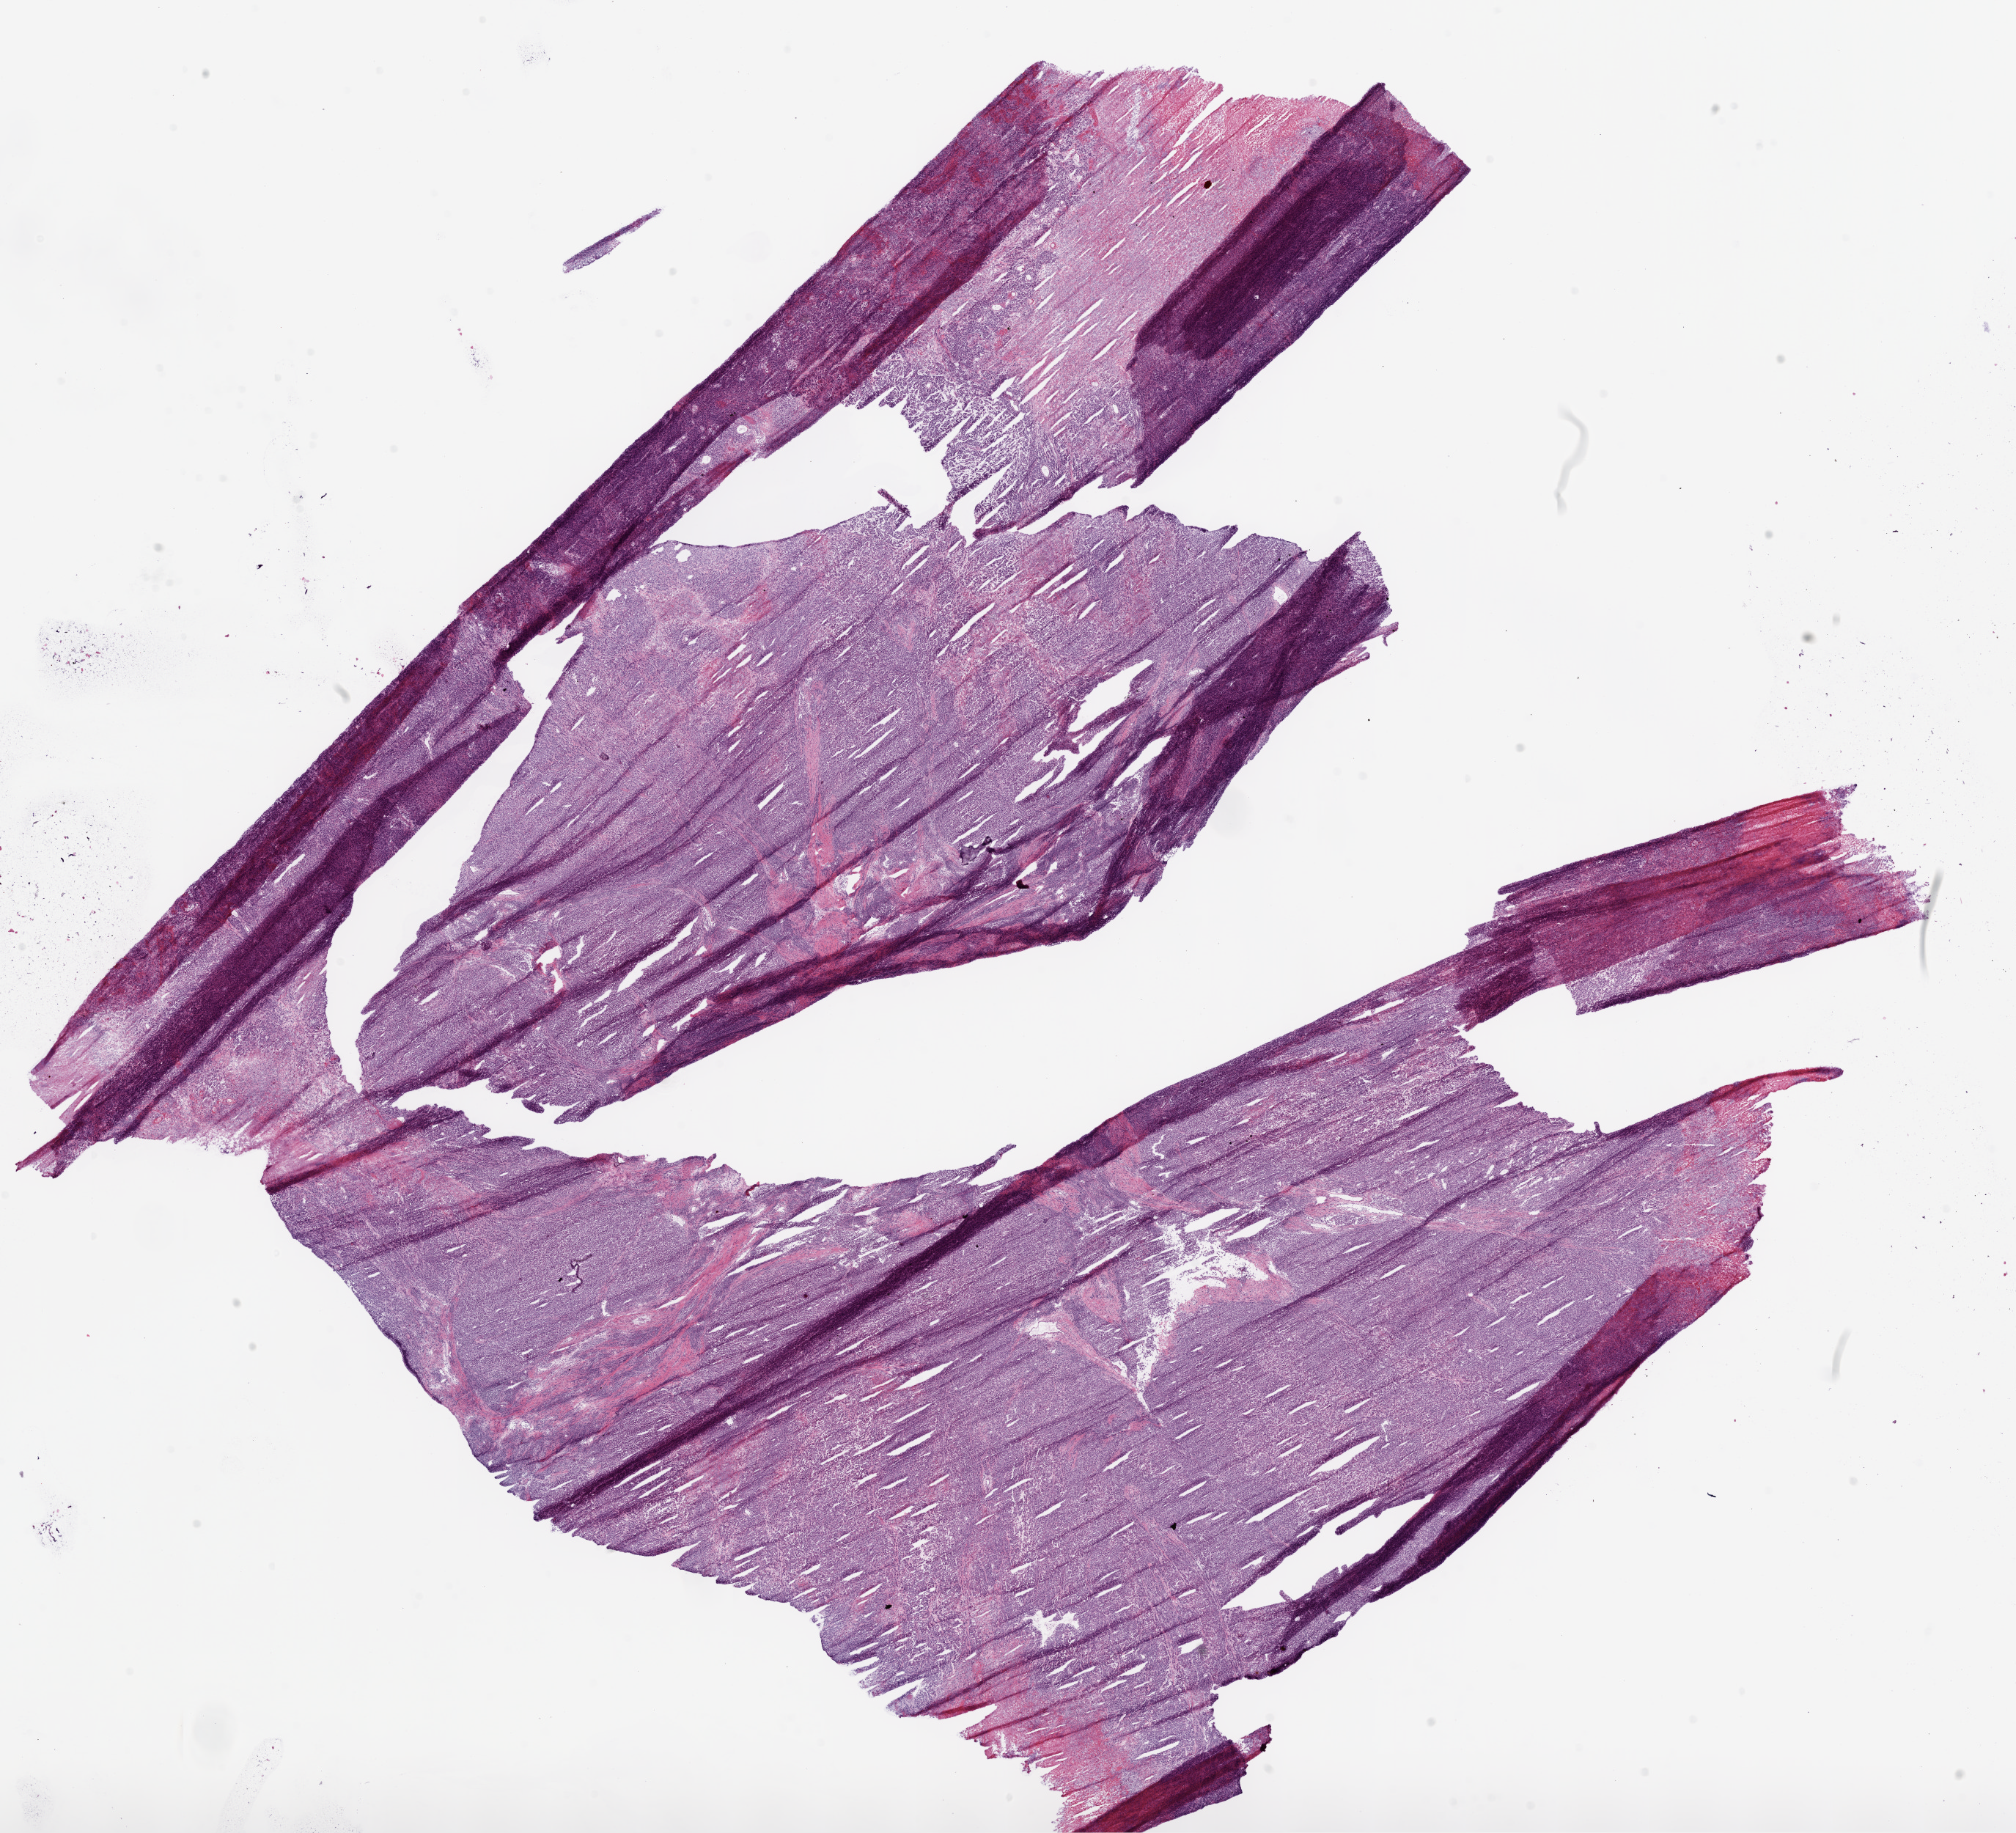
Hematoxylin and eosin (H&E) stained whole-slide image — shown as a low-resolution overview of the whole scanned area (about 22.1 x 20.1 mm, from a 20x scan). Frozen section from the top of the tissue portion. Sample: primary tumour, stomach. Female, age 74 years at initial diagnosis. Histologic grade: G3 (poorly differentiated). Pathologist review of this section (percent, as recorded): tumour cells 85%, tumour nuclei 80%, normal cells 0%, stromal cells 5%, necrosis 10%.
Histologic diagnosis: Adenocarcinoma, NOS.